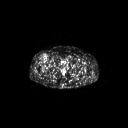
FDG PET of an extremity soft-tissue mass (from a PET/CT study), one axial slice. Slice 310 of 311 in the series (ordered by position). 128 × 128 image matrix. Male patient, age 56 years. From the clinical record (not read from this slice): histological type: pleiomorphic leiomyosarcoma; grade: intermediate; site of the primary tumour: right thigh.
Annotated regions visible in this slice (expert contour drawn on MRI and transferred to this co-registered scan by the dataset authors):
- gross tumour volume including surrounding oedema: box from (x=44, y=56) to (x=47, y=60) px